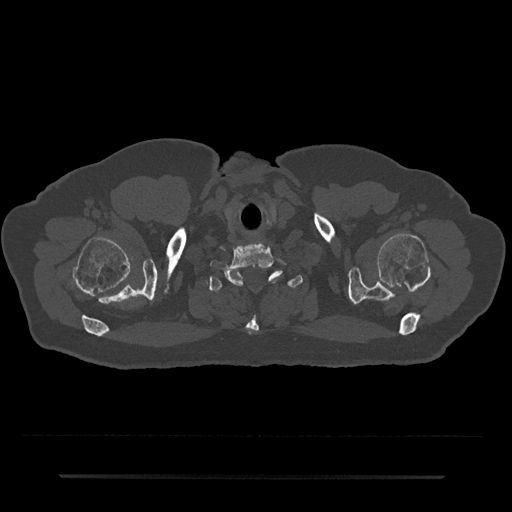
CT including the spine, one axial slice. Position 660 of 797 along the scan axis. Reconstruction kernel Br40s/3. Bone window (W 1800 / L 400 HU). 512 × 512 image matrix, field of view 437 × 437 mm. Male patient, age 69 years. From the clinical record (not read from this slice): primary cancer: prostate.
Structures marked on this image (semi-automatically segmented with operator editing):
- T1 vertebra: bounding box <209,270,303,334> (left, top, right, bottom; pixels)